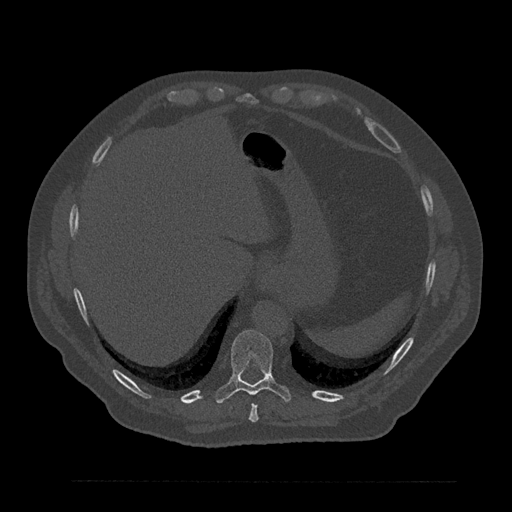
CT including the spine, one axial slice; slice 356 of 797 in the series (ordered by position); reconstruction kernel Br40s/3; 120 kVp; bone window (W 1800 / L 400 HU); 0.5 mm slice thickness; 512 × 512 image matrix, field of view 430 × 430 mm. Patient: male, 61 years. Case-level facts recorded for this patient, not image findings: primary cancer: prostate.
Annotated regions visible in this slice (semi-automatic segmentation, software-assisted and operator-edited):
- T10 vertebra: bounding box <215,330,291,403> (left, top, right, bottom; pixels)
- T9 vertebra: <249,404,259,423>